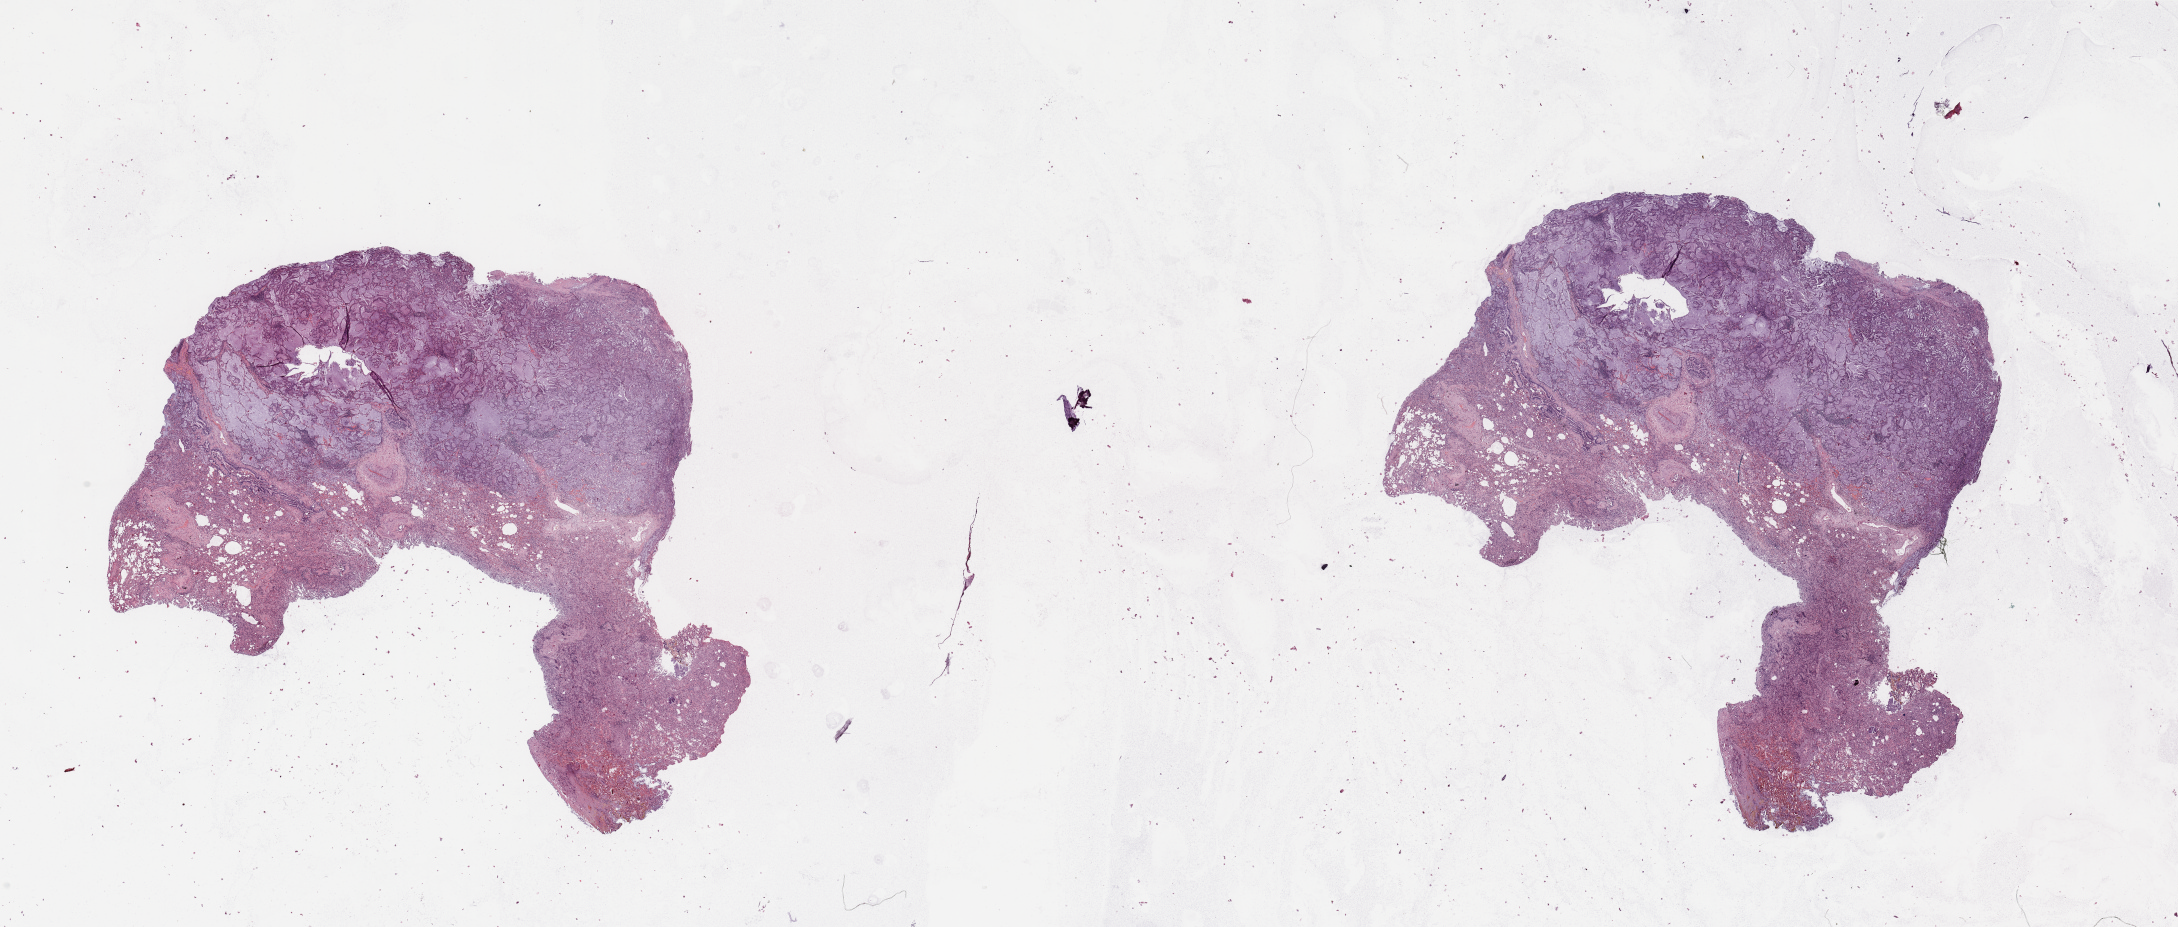
Hematoxylin and eosin (H&E) stained whole-slide image, shown as a low-resolution overview of the whole scanned area (about 34.5 x 14.7 mm, acquisition: 20x scan); tumour tissue sample, lung. Patient: male, age 67 years. Histologic grade: G2 (moderately differentiated).
Diagnosis: Adenocarcinoma, NOS. AJCC pathologic stage: IIA.